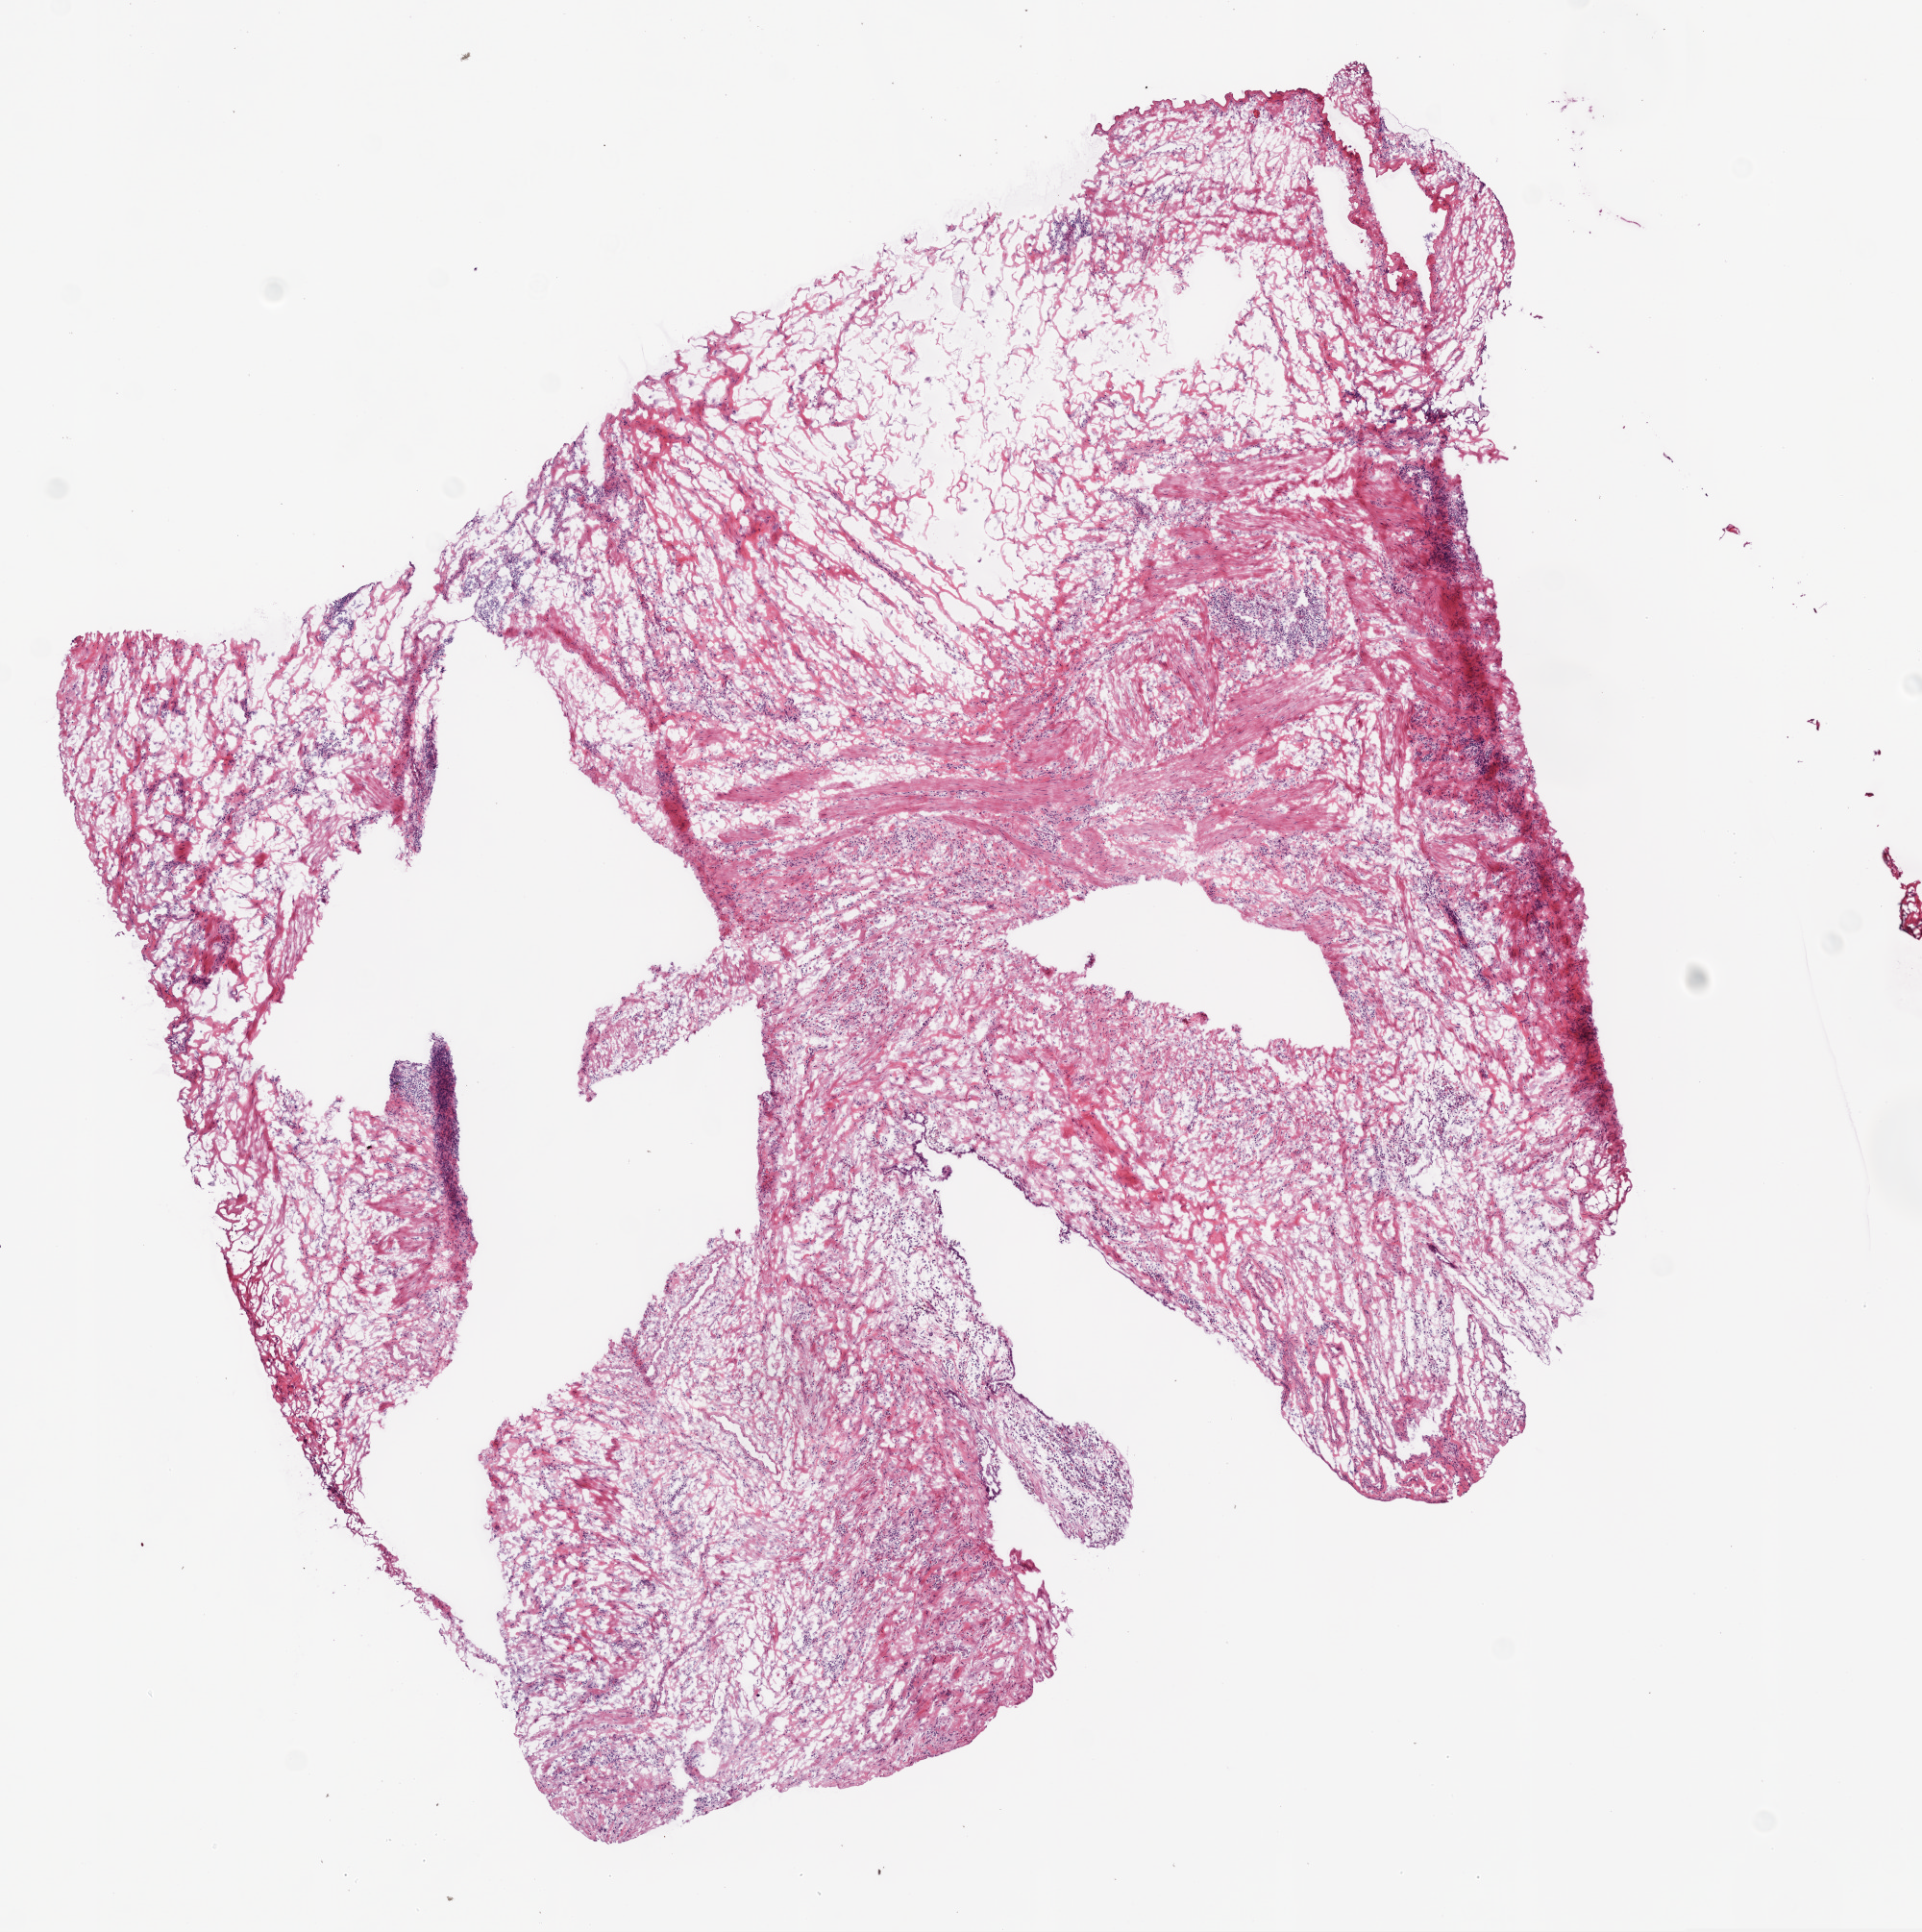
Whole-slide histology image, H&E-stained — low-resolution overview of the scanned area, about 8.0 x 8.1 mm (from a 20x scan), frozen section from the bottom of the tissue portion, sample: solid tissue normal (non-tumour tissue), ovary. Female, age 58 years at initial diagnosis.
This section: solid tissue normal (non-tumour) sample from the same patient. Patient diagnosis: Serous cystadenocarcinoma, NOS.